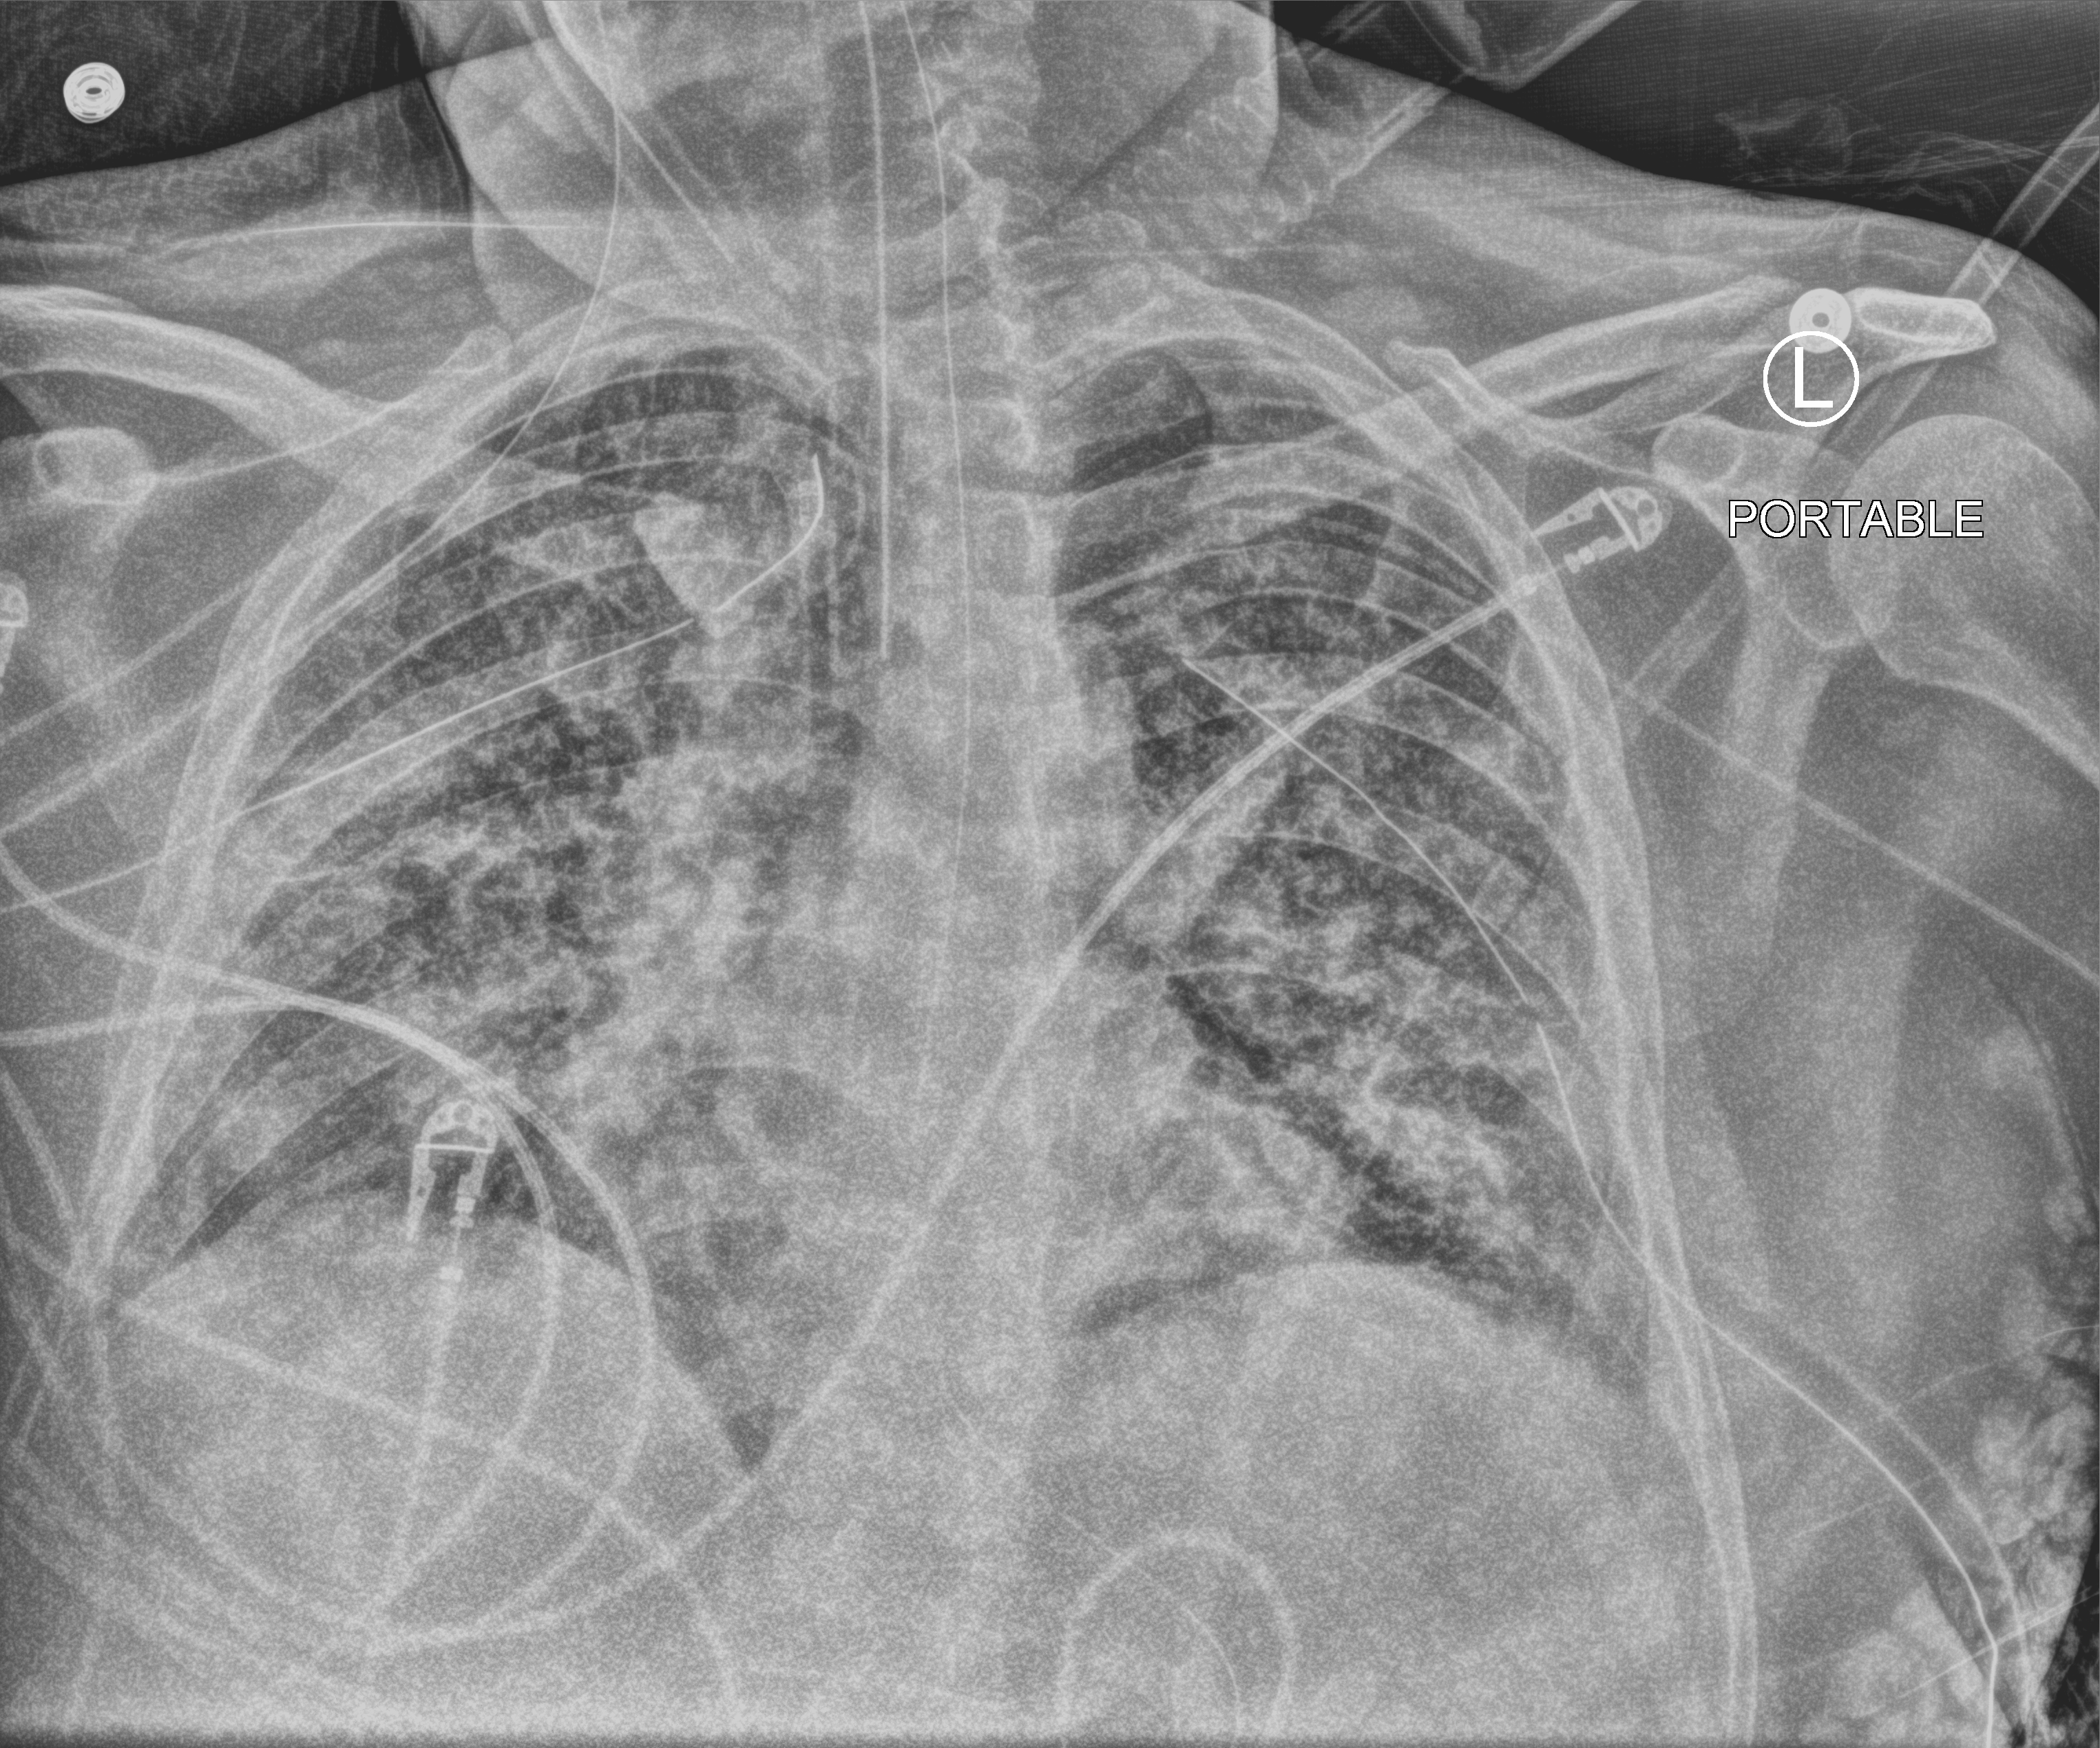
Portable chest radiograph, anteroposterior (AP) projection. Male patient hospitalised with COVID-19, age 18–59 years.
Admission-level facts for this patient (not findings on this image; timing relative to this image not recorded): smoking status (admission record): never; admitted to intensive care during this hospital stay: yes; diabetes (admission record): yes.